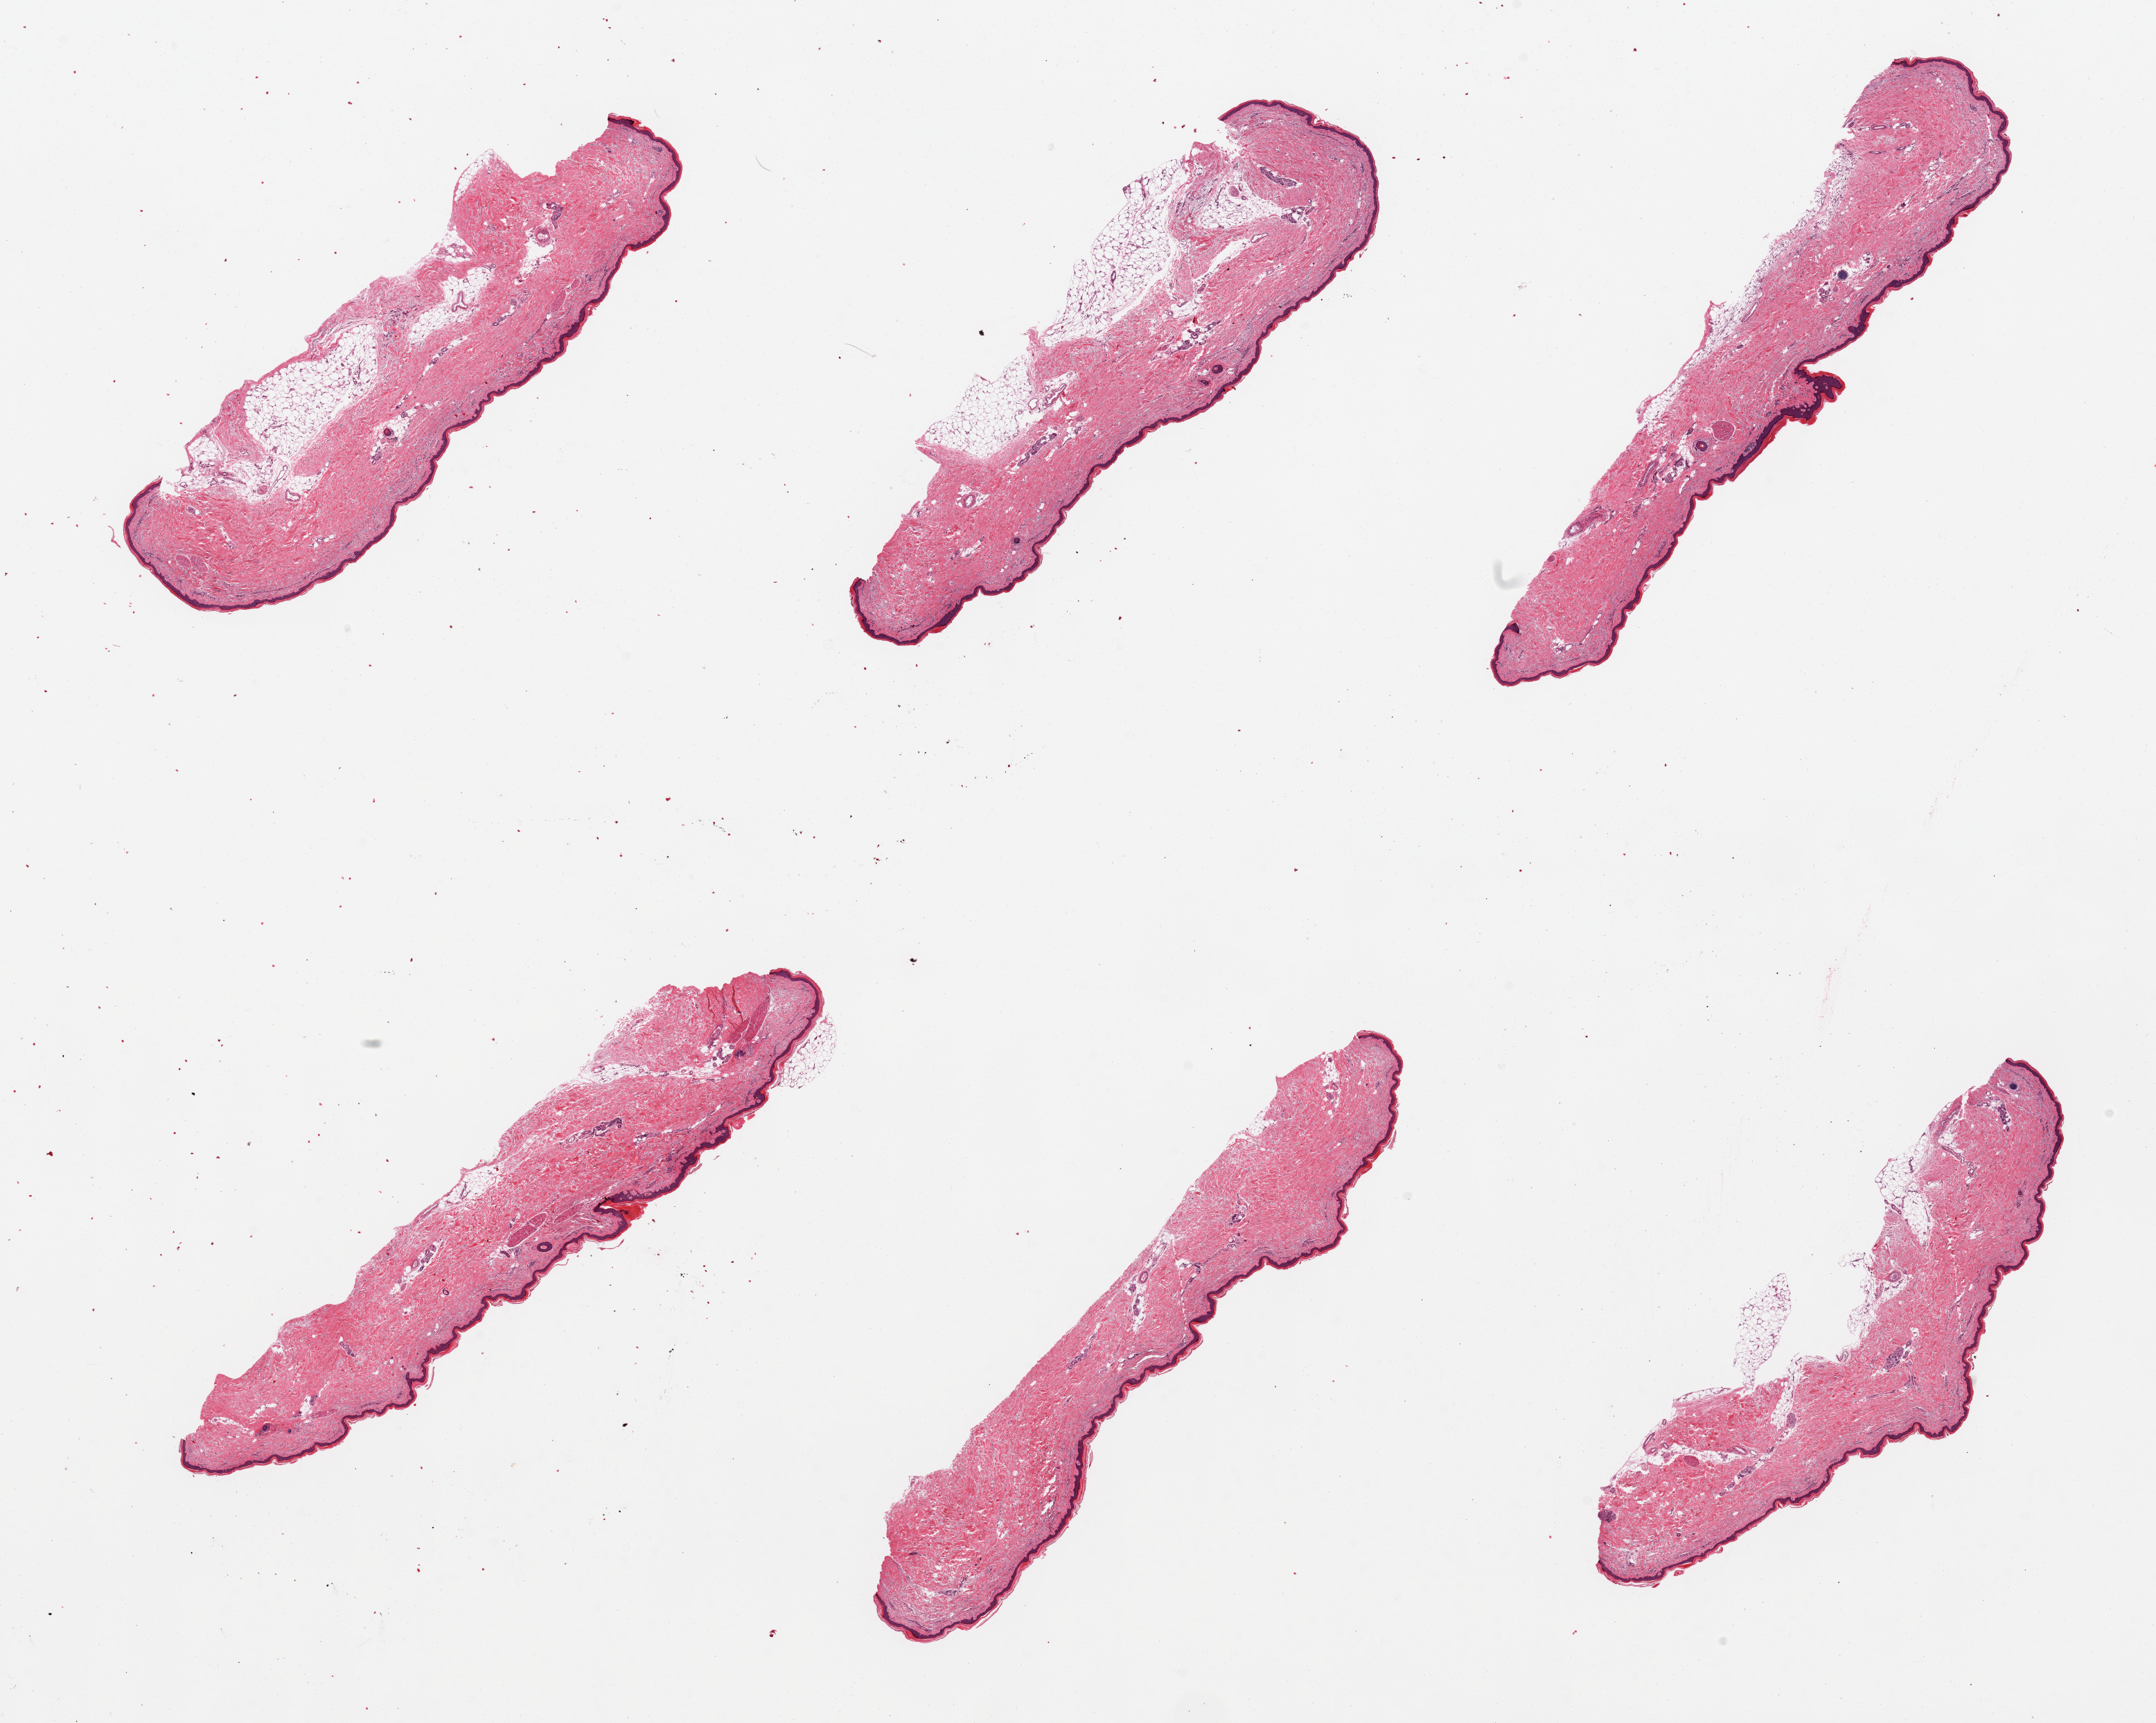
Whole-slide image, hematoxylin and eosin (H&E) stain — a low-resolution overview of the entire scanned area, about 24.6 x 19.7 mm. PAXgene-fixed, paraffin-embedded tissue. Sampled site (target tissue): skin of lower leg. Donor tissue sample. Donor sex: female.
Pathologist's review note for this sample: 6 pieces, focal adherent dermal fat.